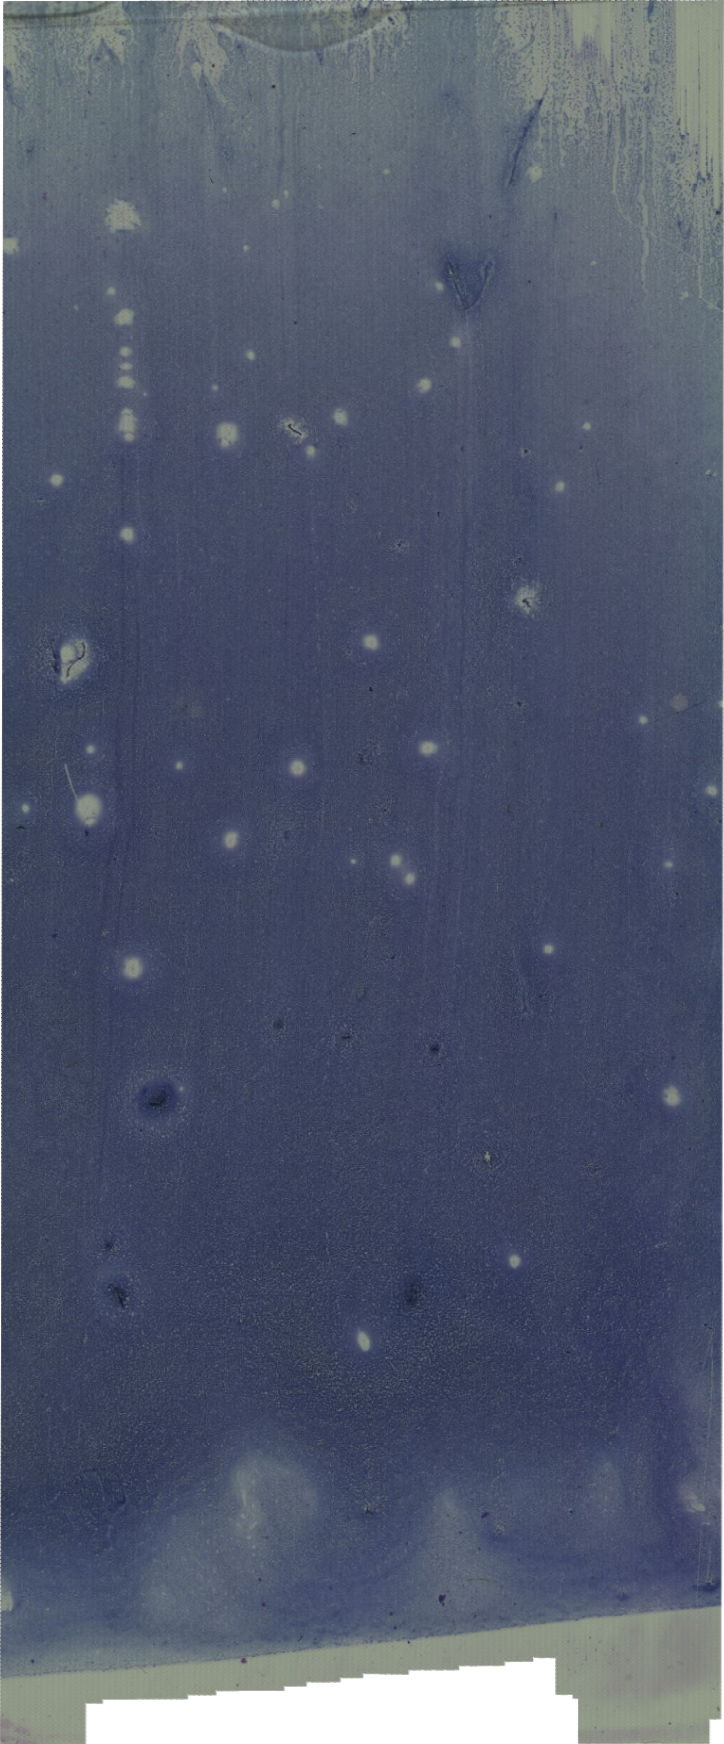
Bone marrow aspirate smear, May-Grünwald-Giemsa (MGG) stain, whole-slide image — low-resolution overview of the scanned area, about 20.5 x 49.4 mm. Male patient.
- diagnosis: Acute Megakaryoblastic Leukemia